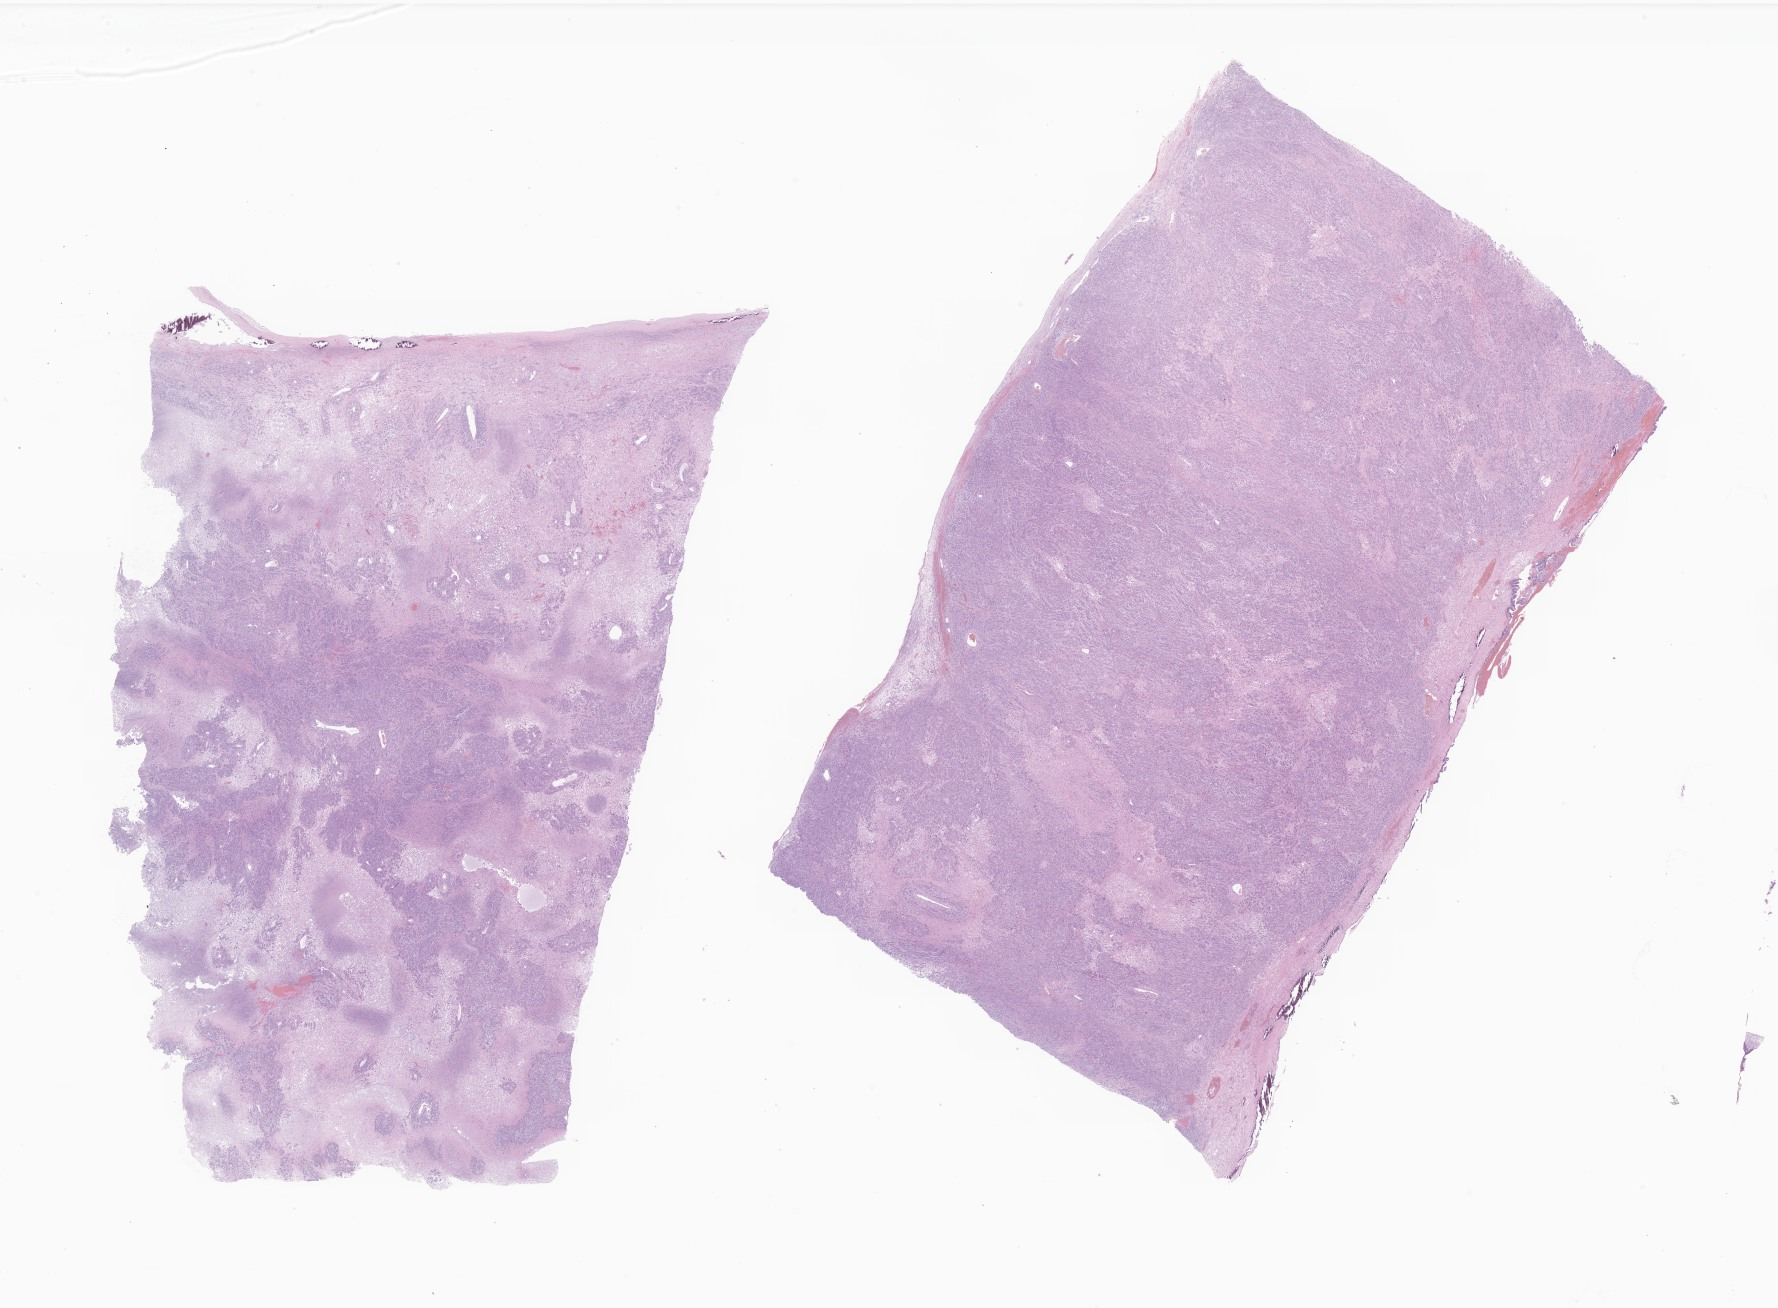
Whole-slide image, H&E stain of tumor tissue from the ovary, shown as a low-resolution overview of the whole scanned area (about 30.0 x 22.1 mm). Formalin-fixed, paraffin-embedded (FFPE) tissue. Patient female; age 152 months (12 years 8 months).
* recorded diagnosis: Carcinoma, NOS